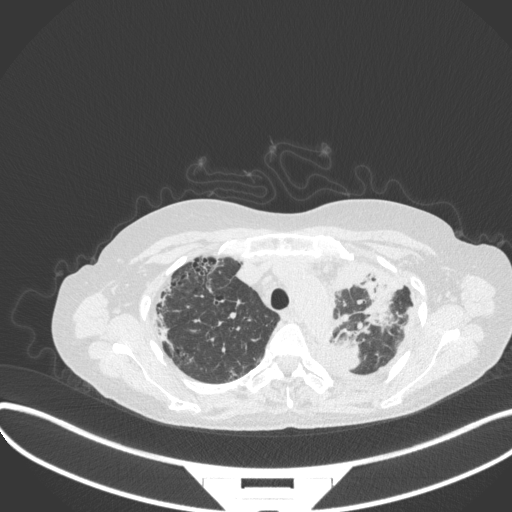
Chest CT, one axial slice; position 267 of 373 along the scan axis; lung window (W 1500 / L -600 HU); 1 mm slice thickness; 512 × 512 image matrix, field of view 400 × 400 mm. Patient: female, 56 years. Case-level facts recorded for this patient, not image findings: clinical TNM (as recorded): T1 N0 M0.
Outlined on this slice (bounding box drawn by a radiologist):
- lung tumour (recorded histology: adenocarcinoma): bounding box <326,328,369,377> (left, top, right, bottom; pixels)
- lung tumour (recorded histology: adenocarcinoma): <355,261,403,324>